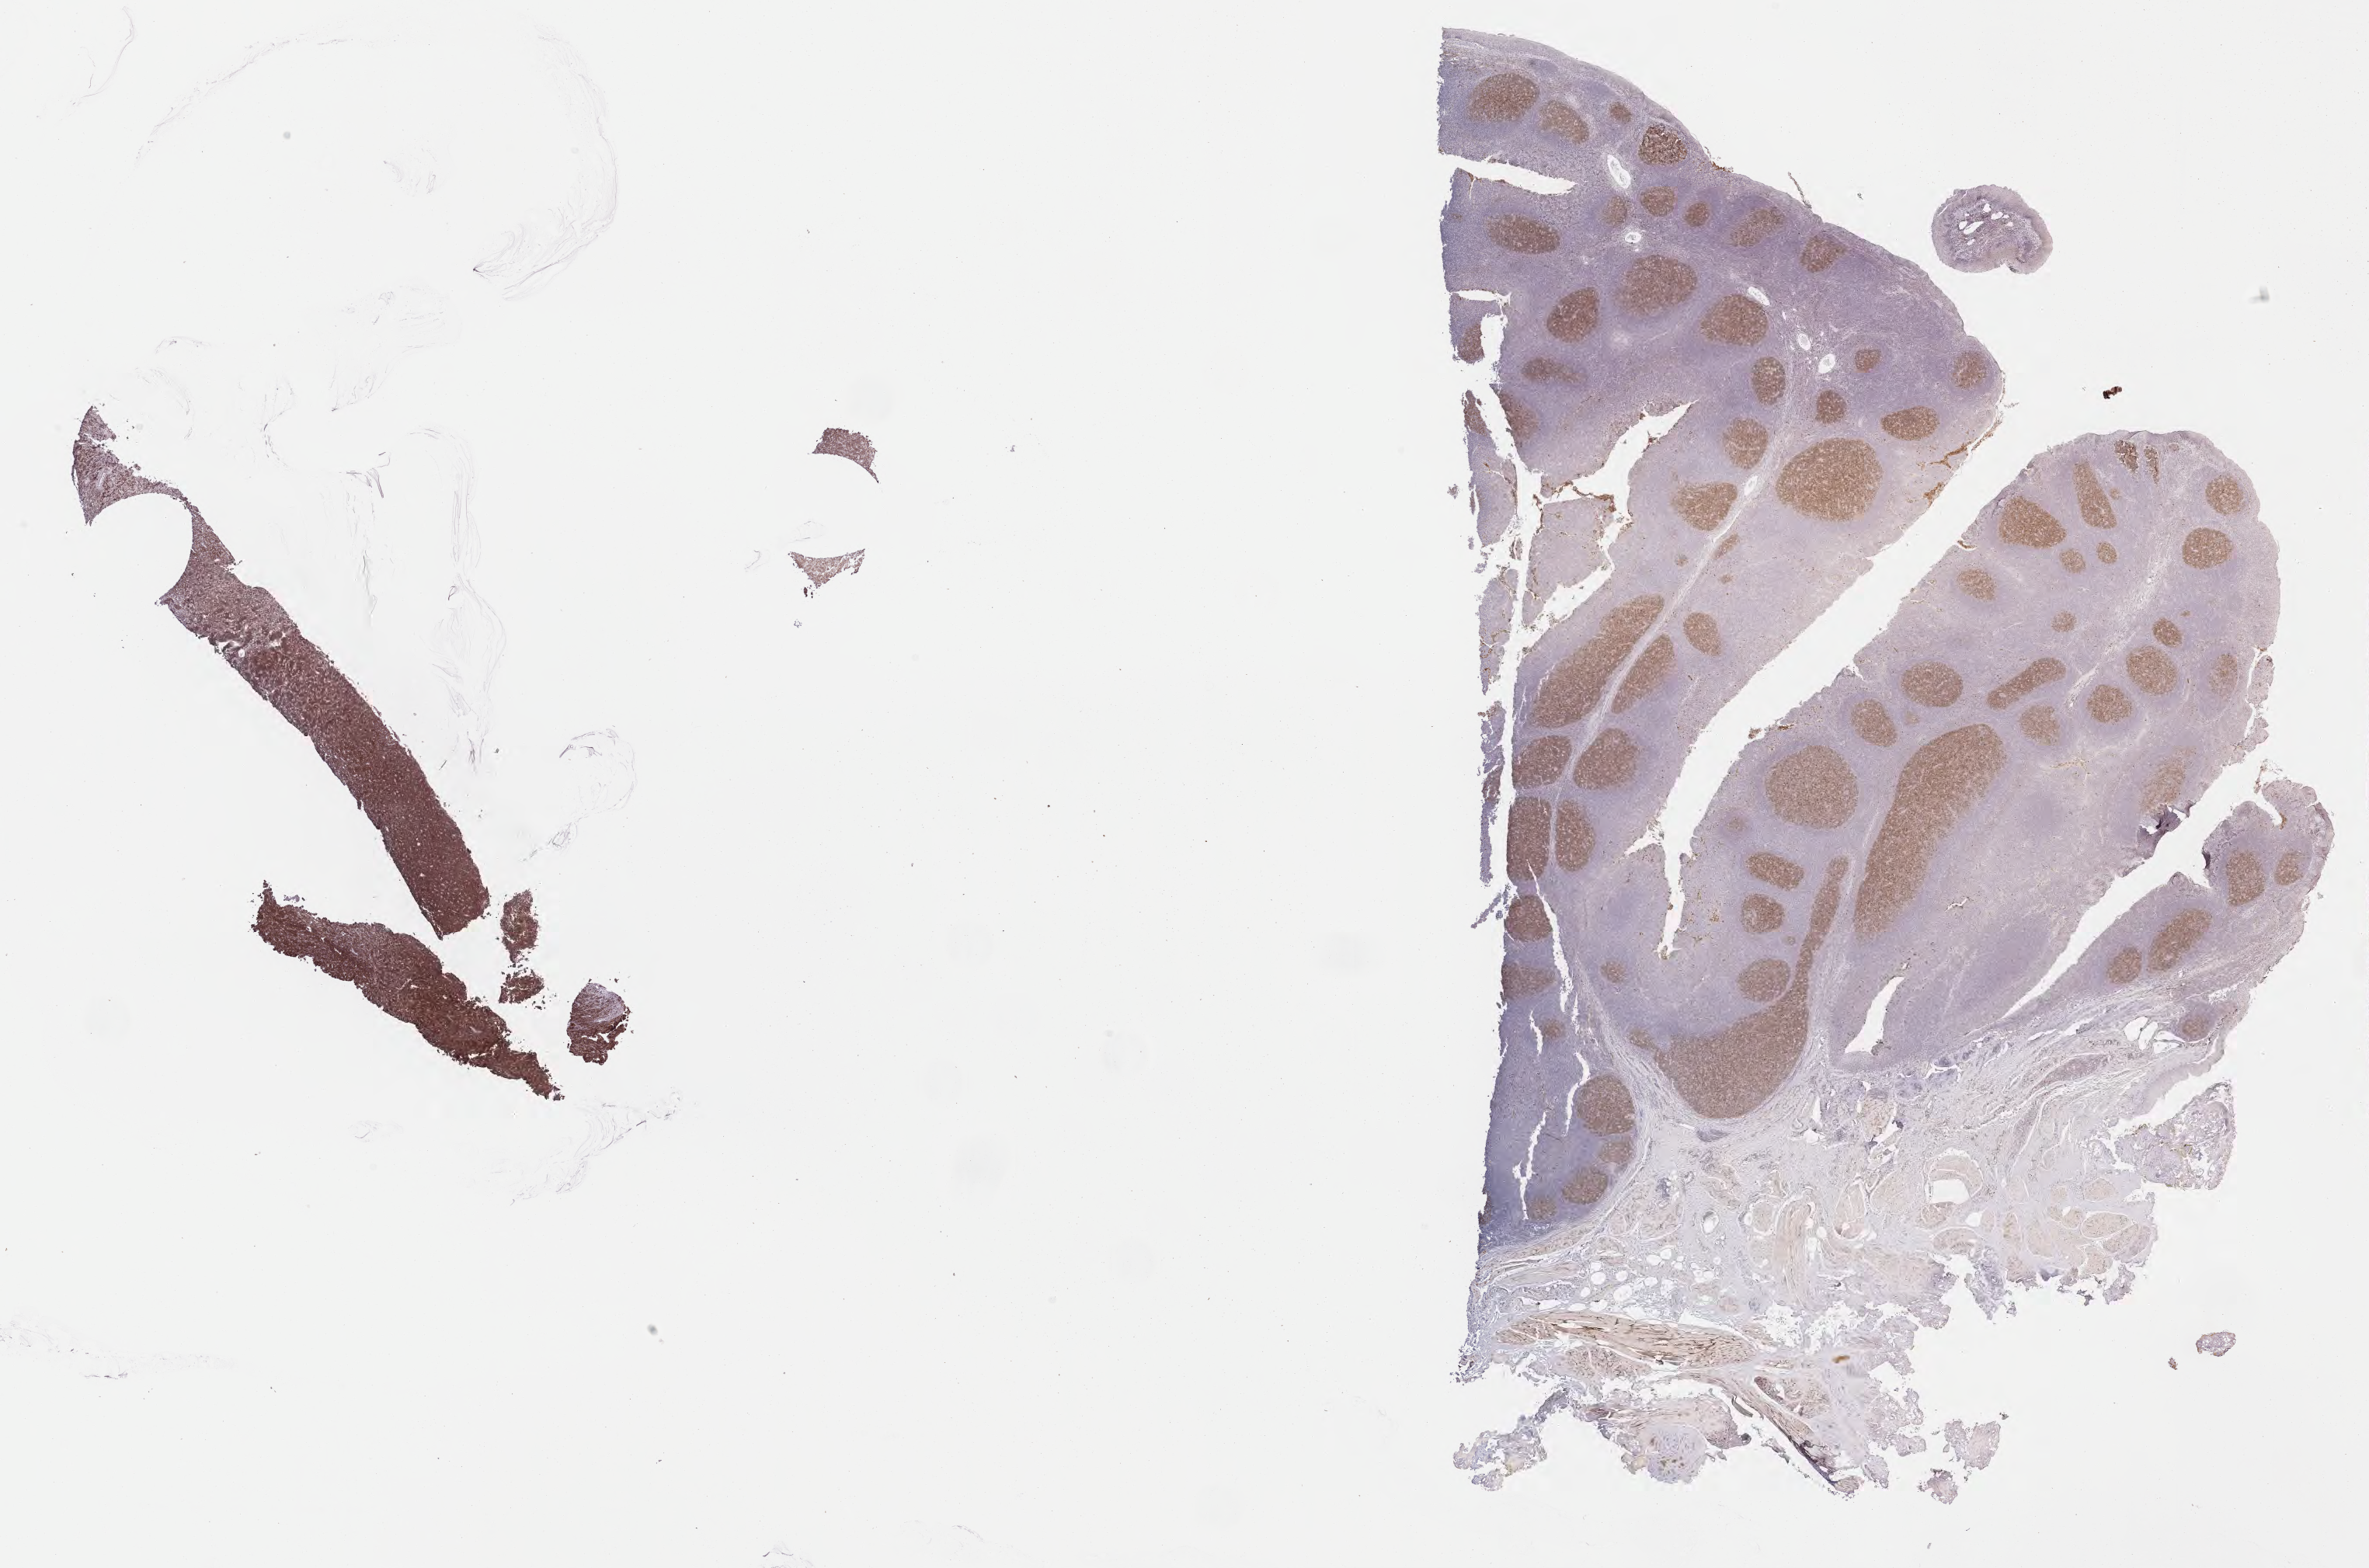
IHC for CD10, whole-slide image, whole scanned area (about 24.7 x 16.3 mm) shown as a low-resolution overview; specimen: tumor tissue; anatomic site: liver. Patient: male, 15 years old.
Diagnosis: Burkitt lymphoma, NOS.